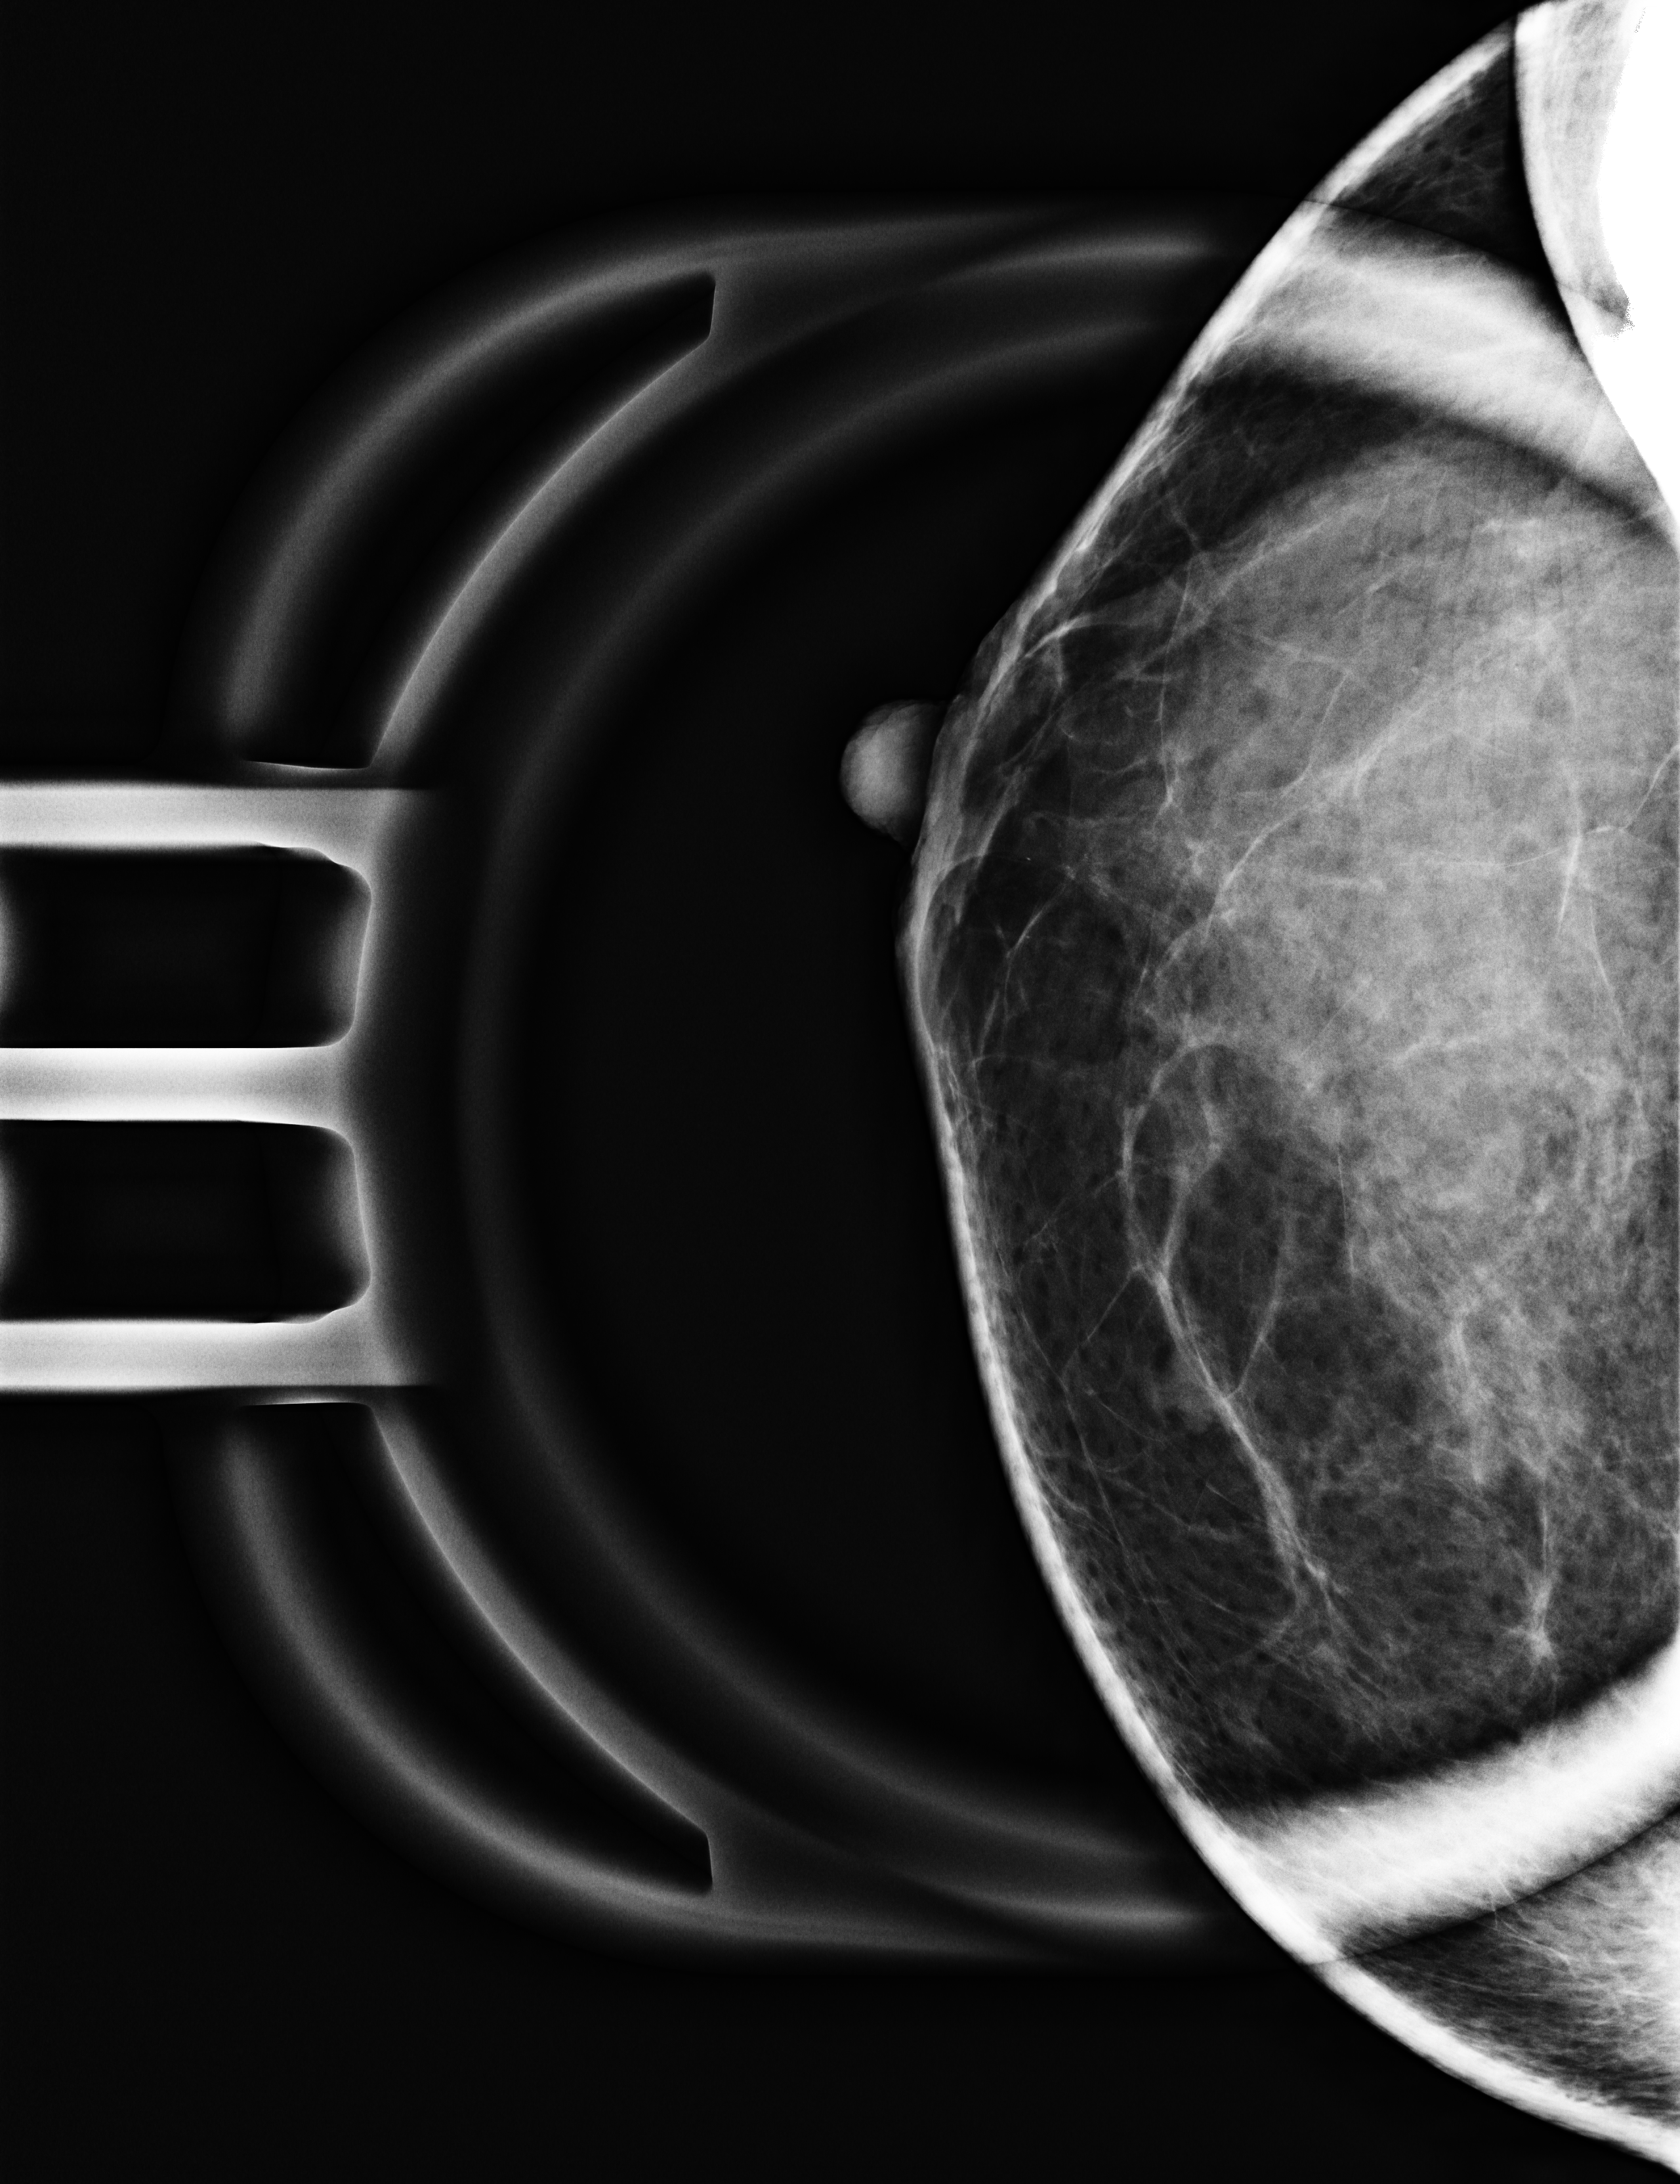
Additional (diagnostic) view; compressed breast thickness 28 mm; system: Selenia Dimensions. Female patient, age 58 years.
Image type: full-field digital mammogram. Breast: right. Projection: craniocaudal (CC) view, magnification.